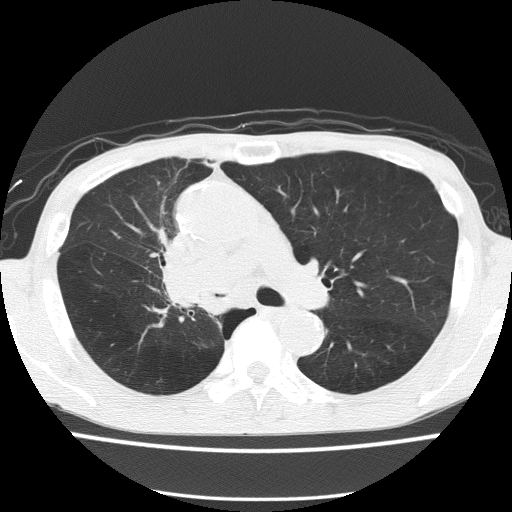
Low-dose screening chest CT, axial slice, first (baseline) screen, lung window (W 1500 / L -600 HU), lung (sharp) reconstruction kernel (FC51), slice 57 of 150 in the series, 512 × 512 image matrix, field of view 336 × 336 mm. Male participant, aged 59 years at enrolment.
Expert reader's lesion annotation, box from (x=142, y=230) to (x=232, y=321) px. The screening reader recorded 5 non-calcified nodules or masses ≥4 mm on this exam (left upper lobe, left upper lobe, left upper lobe, right middle lobe, right lower lobe); which of them this box marks is not recorded.